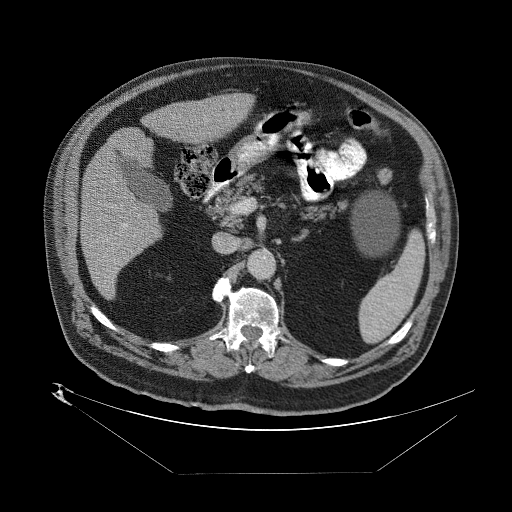
Contrast-enhanced abdominal CT (liver protocol), one axial slice. Position 34 of 89 along the scan axis. Reconstruction kernel STANDARD. 140 kVp. One of 2 acquisitions stored at this slice position. Soft-tissue window (W 400 / L 40 HU). 2.5 mm slice thickness. 512 × 512 image matrix, field of view 480 × 480 mm. From the clinical record (not read from this slice): diagnosis: hepatocellular carcinoma (patient treated with transarterial chemoembolisation; whether this scan precedes or follows treatment is not stated here); TNM stage (as recorded): Stage-II; Child-Pugh class: B; tumour differentiation: moderately differentiated; tumour size: 4 cm.
Outlined on this slice (semi-automatically segmented with operator editing):
- abdominal aorta: bounding box [x1, y1, x2, y2] px = [247, 250, 275, 280]
- liver parenchyma outside the tumour (the mass and vessels are separate outlines, so this box may not span the whole liver): [80, 92, 248, 302]
- liver vessels: [99, 213, 139, 246]